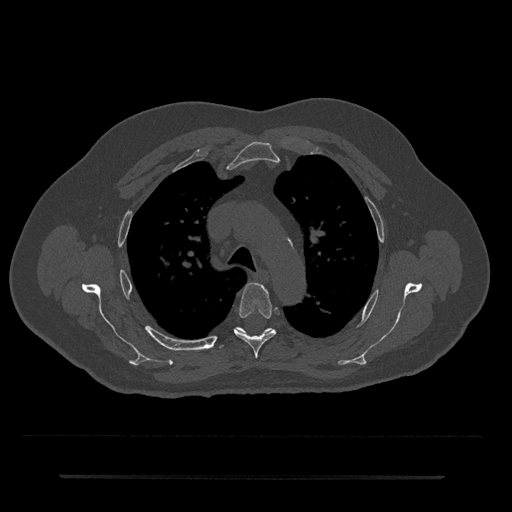
CT including the spine, one axial slice. Position 520 of 797 along the scan axis. Reconstruction kernel Br40s/3. 120 kVp. Bone window (W 1800 / L 400 HU). 512 × 512 image matrix, field of view 437 × 437 mm. Patient: male, 69 years. From the clinical record (not read from this slice): primary cancer: prostate.
Structures marked on this image (semi-automatically segmented with operator editing):
- T4 vertebra: box from (x=234, y=283) to (x=276, y=359) px
- T5 vertebra: (x=219, y=327)–(x=273, y=349)